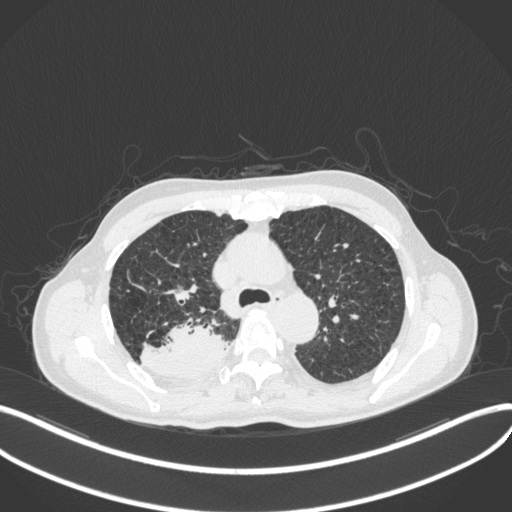
Chest CT, one axial slice; slice 315 of 423 in the series (ordered by position); lung window (W 1500 / L -600 HU); 1 mm slice thickness; 512 × 512 image matrix, field of view 400 × 400 mm. Male patient, age 79 years. Case-level facts recorded for this patient, not image findings: clinical TNM (as recorded): T3 N0 M0.
Structures marked on this image (bounding box drawn by a radiologist):
- lung tumour (recorded histology: adenocarcinoma): bounding box <142,320,234,380> (left, top, right, bottom; pixels)